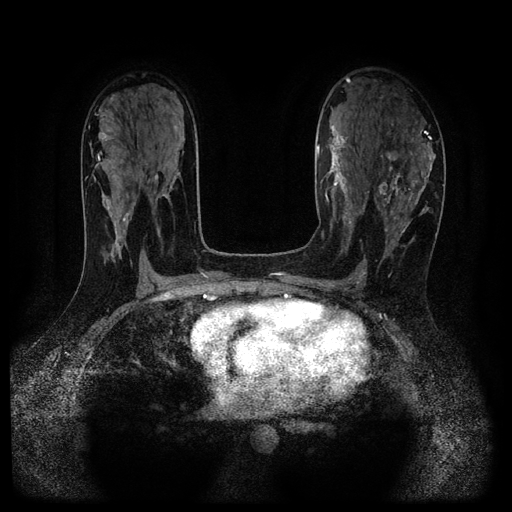
Breast MRI (dynamic contrast-enhanced, multi-phase), one axial slice; position 62 of 116 along the scan axis; dynamic contrast-enhanced series, time point 2 of 5 at this slice position (early post-contrast); 1.5 T; TE 2.7 ms, TR 5.4 ms; 512 × 512 image matrix, field of view 330 × 330 mm. Patient: female, 43 years.
Annotated regions visible in this slice (semi-automatic segmentation, software-assisted and operator-edited):
- breast lesion (labelled 'tumour' in the annotation; benign lesions carry a separate 'benign' label): box from (x=375, y=127) to (x=436, y=234) px
- breast lesion (labelled benign in the annotation): (x=320, y=125)–(x=358, y=234)